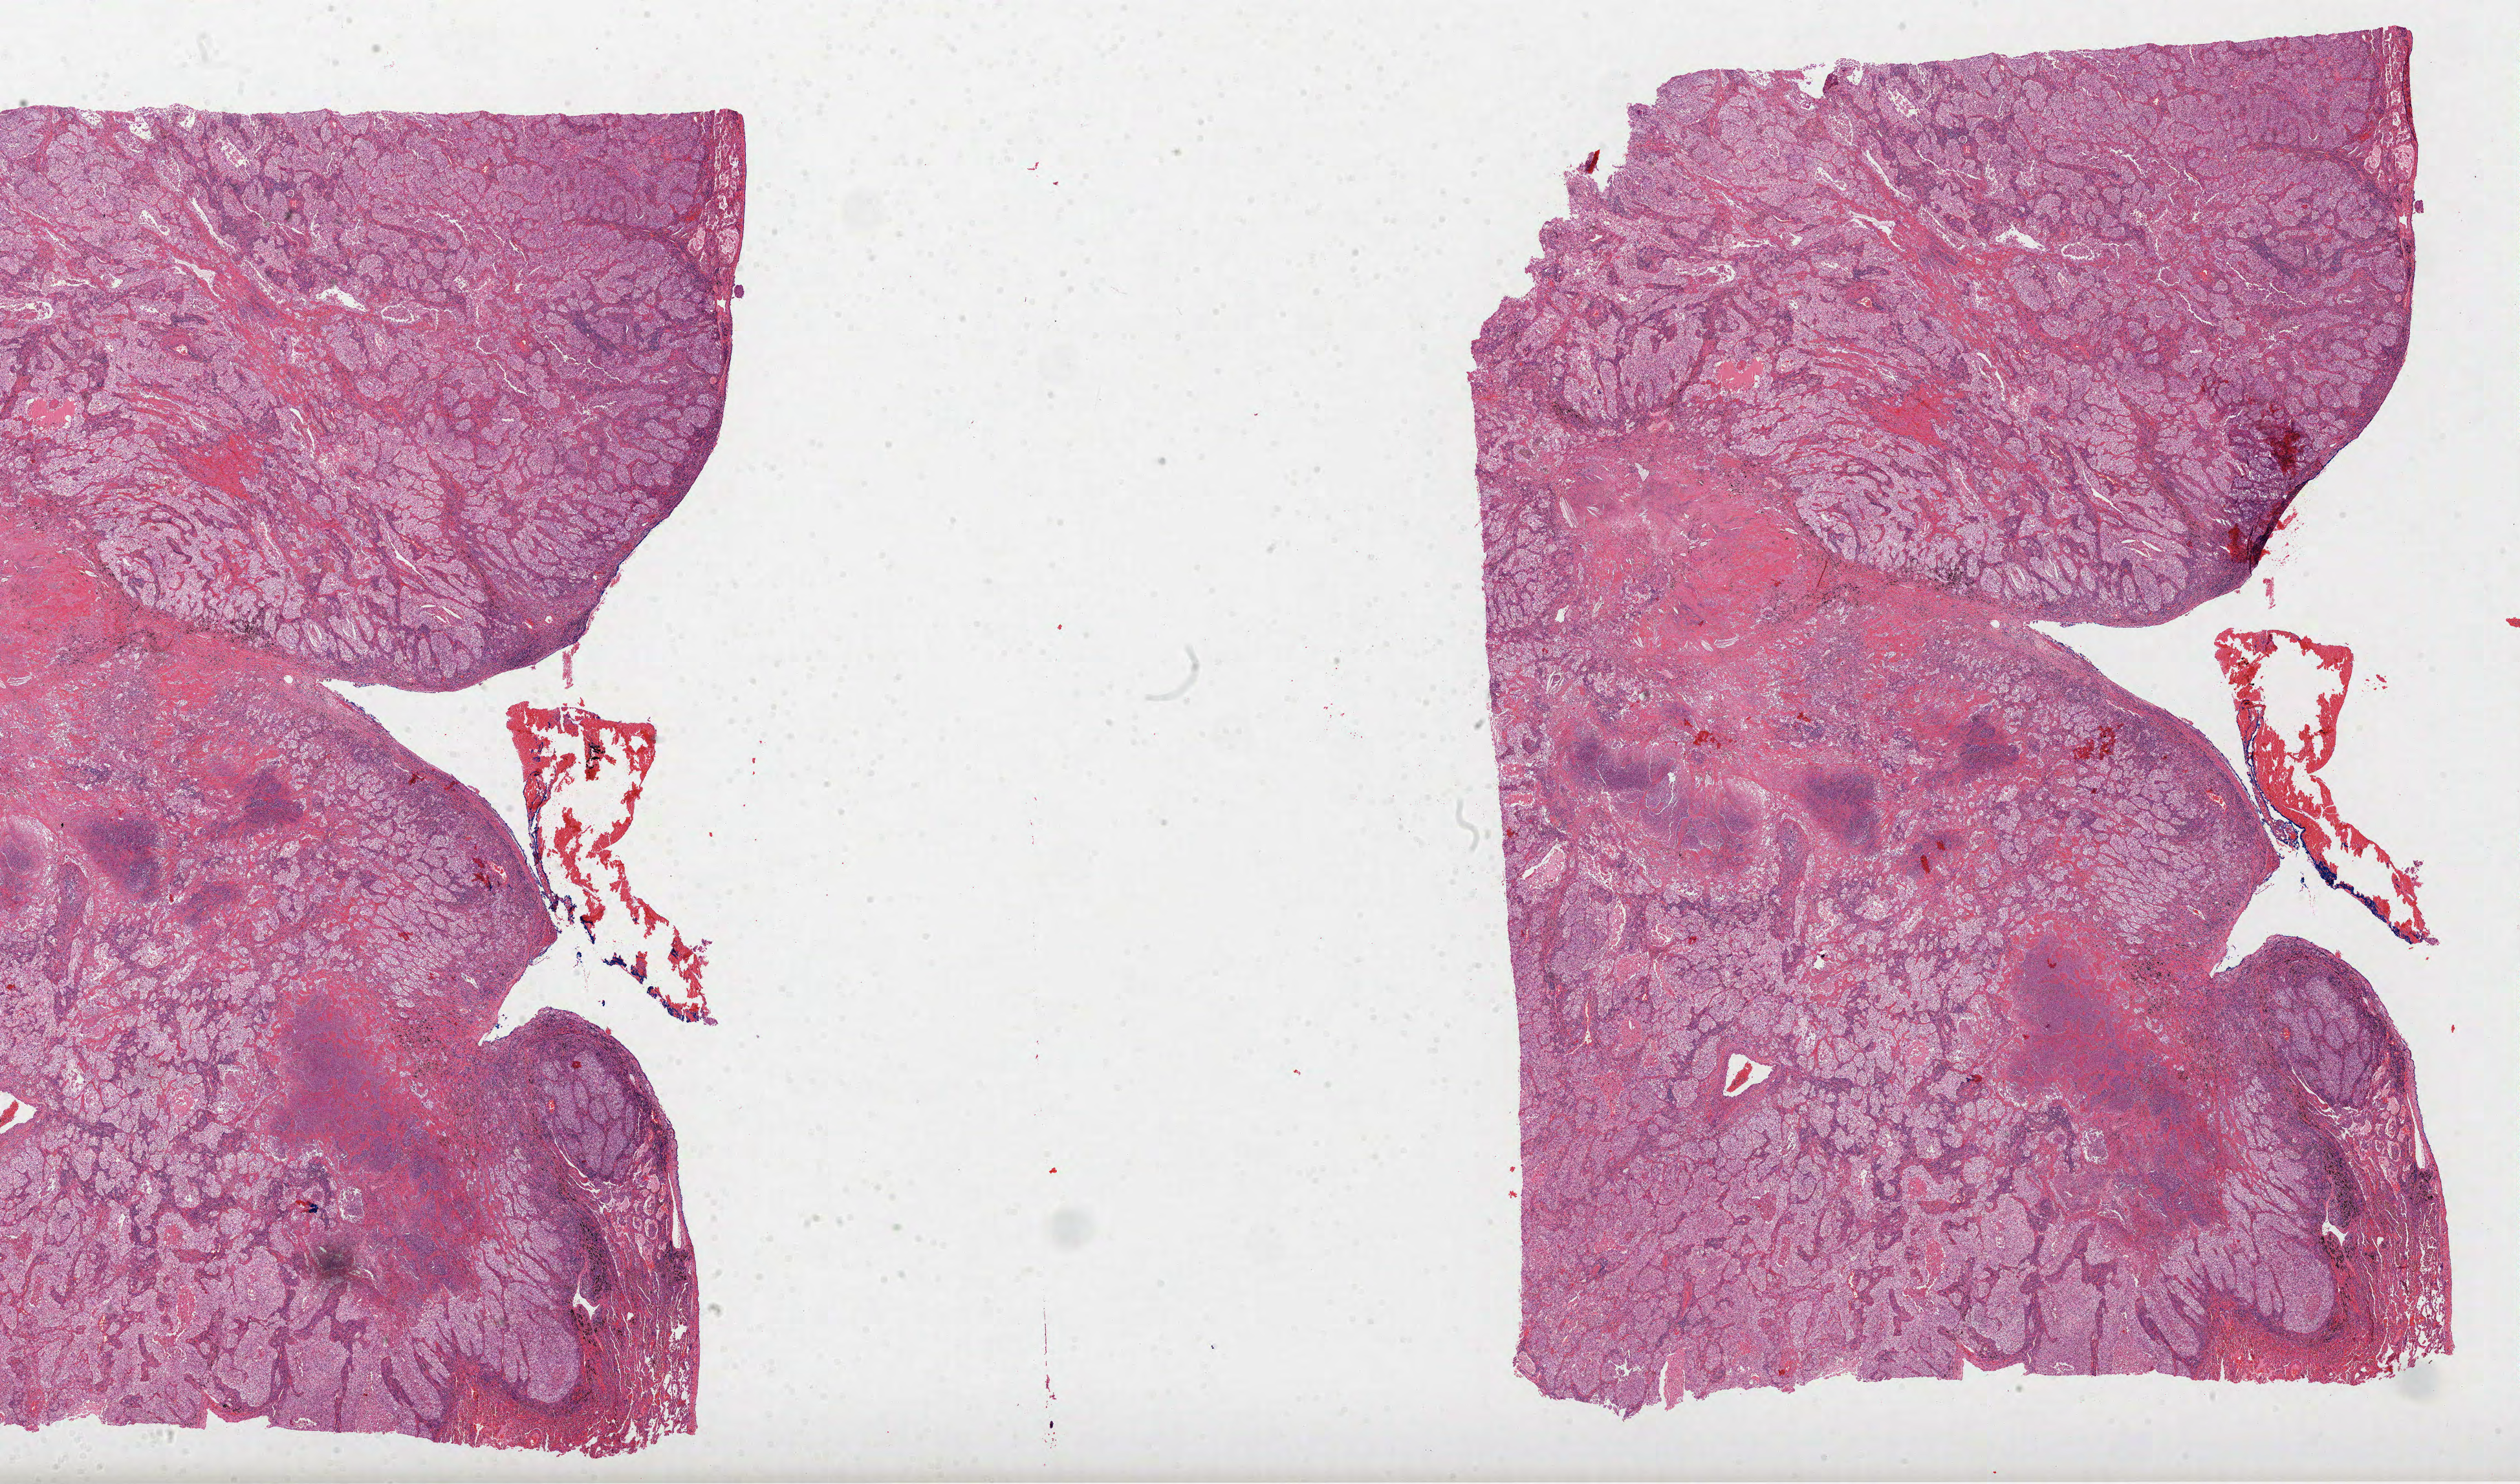
Digitized H&E tissue section (whole slide), whole scanned area (about 31.4 x 18.5 mm) shown as a low-resolution overview. Formalin-fixed paraffin-embedded (FFPE) diagnostic section. Sample: primary tumour, lung. Patient: male, age at initial diagnosis 59 years.
• AJCC pathologic stage: IIB (7th edition)
• TNM: T2b N1 MX
• pathologic diagnosis: Adenocarcinoma with mixed subtypes (upper lobe, lung)